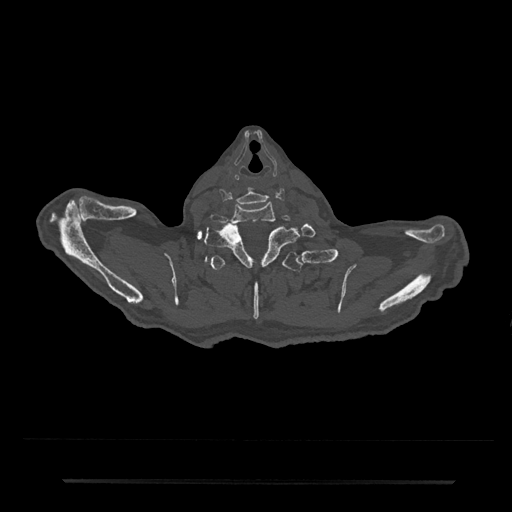
CT including the spine, one axial slice. Slice 720 of 797 in the series (ordered by position). Reconstruction kernel Br40s/3. 120 kVp. Bone window (W 1800 / L 400 HU). 0.5 mm slice thickness. 512 × 512 image matrix, field of view 427 × 427 mm. Patient: male, 74 years. Case-level facts recorded for this patient, not image findings: primary cancer: prostate.
Structures marked on this image (semi-automatic segmentation, software-assisted and operator-edited):
- T1 vertebra: bounding box (x1, y1, x2, y2) in pixels: (203, 222, 299, 267)
- T2 vertebra: (202, 251, 314, 320)